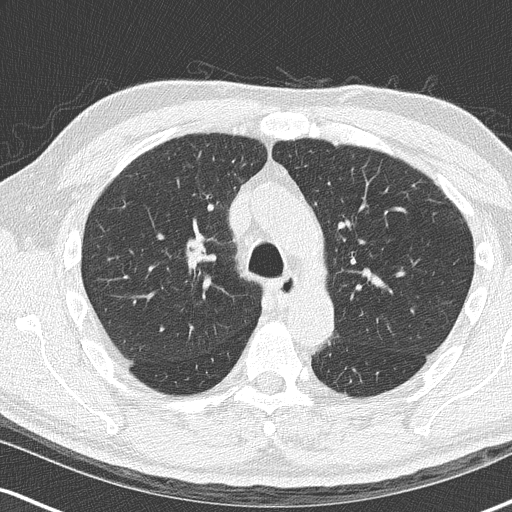
Low-dose screening chest CT, axial slice. Second screening round (one year after baseline). Lung window (W 1500 / L -600 HU). 512 × 512 image matrix, field of view 320 × 320 mm. Male, age 68 years at enrolment.
Expert-annotated lung lesion, bounding box <151,221,218,286> (left, top, right, bottom; pixels). The exam's reader record, not a measurement of the box and not confirmed to be the same lesion: non-calcified nodule or mass ≥4 mm, right upper lobe, 18 × 15 mm, smooth margins, soft tissue attenuation, pre-existing on the prior screen: no. Official screen result: positive, change unspecified: nodule(s) >= 4 mm or enlarging nodule(s), mass(es), or other non-specific abnormalities suspicious for lung cancer. Participant outcome: lung cancer diagnosed 136 days after this screen — small cell carcinoma, NOS, right upper lobe, stage IIIB (AJCC 6th edition), 20 mm at pathology.